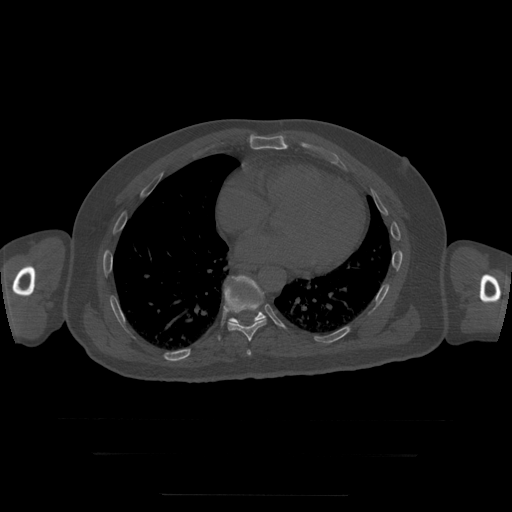
CT including the spine, one axial slice; position 139 of 397 along the scan axis; reconstruction kernel STANDARD; bone window (W 1800 / L 400 HU); 512 × 512 image matrix. Patient age 73 years. From the clinical record (not read from this slice): primary cancer: prostate.
Outlined on this slice (semi-automatic segmentation, software-assisted and operator-edited):
- T10 vertebra: bounding box [x1, y1, x2, y2] px = [226, 275, 266, 324]
- T8 vertebra: [247, 350, 252, 356]
- T9 vertebra: [218, 287, 267, 341]